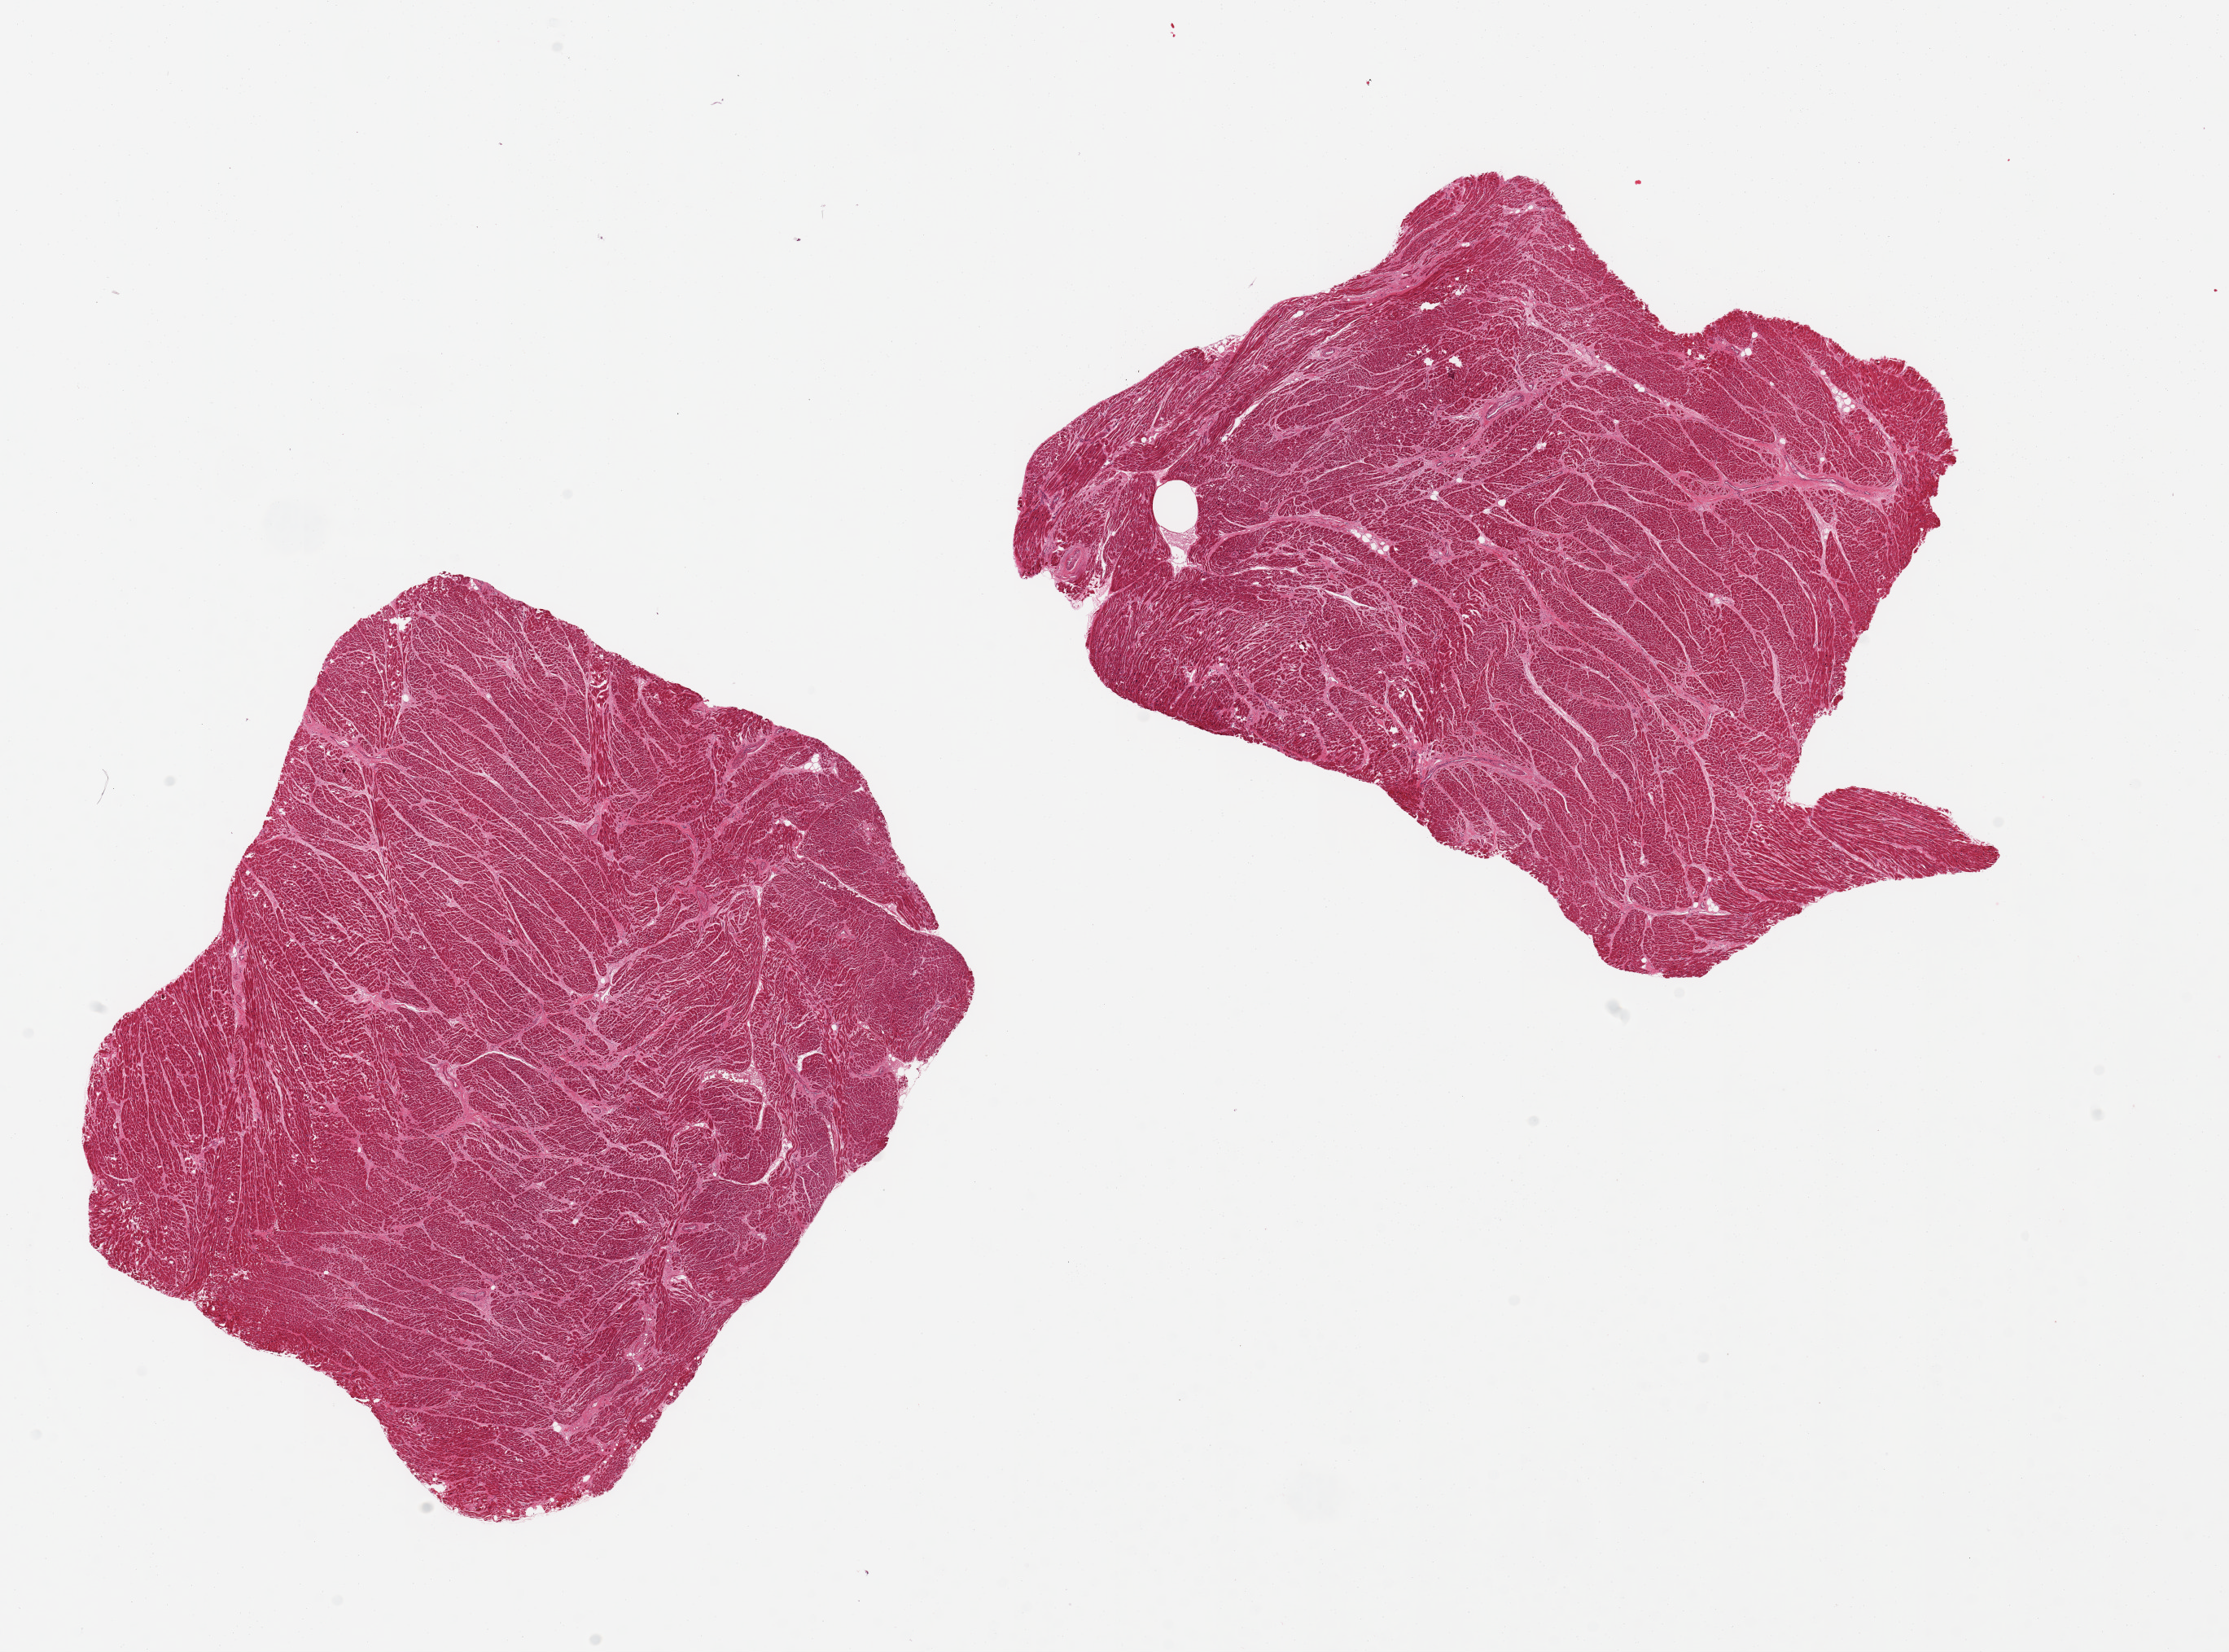
Hematoxylin and eosin (H&E) whole-slide image, brightfield, whole scanned area (about 21.7 x 16.0 mm) shown as a low-resolution overview; PAXgene-fixed, paraffin-embedded tissue; target tissue: heart; tissue donor sample. Donor sex: female.
Reviewer comment on this tissue sample: 2 pieces, increased interstitial fibrosis.